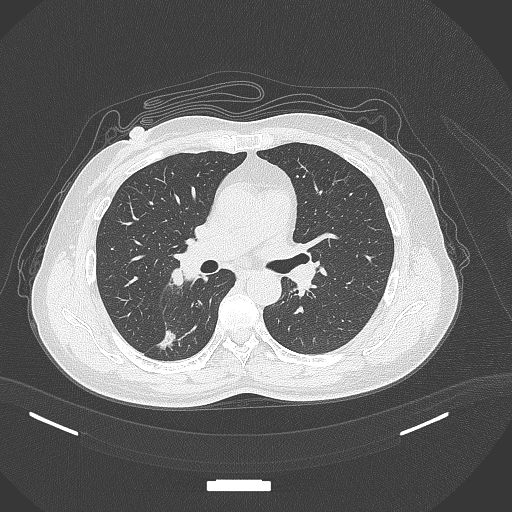
Chest CT, one axial slice; slice 176 of 352 in the series (ordered by position); 120 kVp; lung window (W 1500 / L -600 HU); 512 × 512 image matrix. Patient: female, 55 years. Case-level facts recorded for this patient, not image findings: clinical TNM (as recorded): T1c N1 M0.
Outlined on this slice (bounding box drawn by a radiologist):
- lung tumour (recorded histology: adenocarcinoma): bounding box <155,326,180,357> (left, top, right, bottom; pixels)